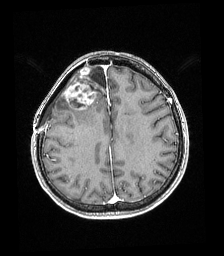
Brain MRI from a brain-tumour surgery series, one axial slice; position 67 of 192 along the scan axis; T1-weighted post-contrast; 1 mm slice thickness; 224 × 256 image matrix, field of view 219 × 250 mm. Case-level facts recorded for this patient, not image findings: histopathology: Astrocytoma; WHO grade: 4; IDH mutation: yes; tumour location: Right superficial frontal.
Outlined on this slice (manually delineated by an expert):
- tumour: box from (x=65, y=65) to (x=94, y=111) px